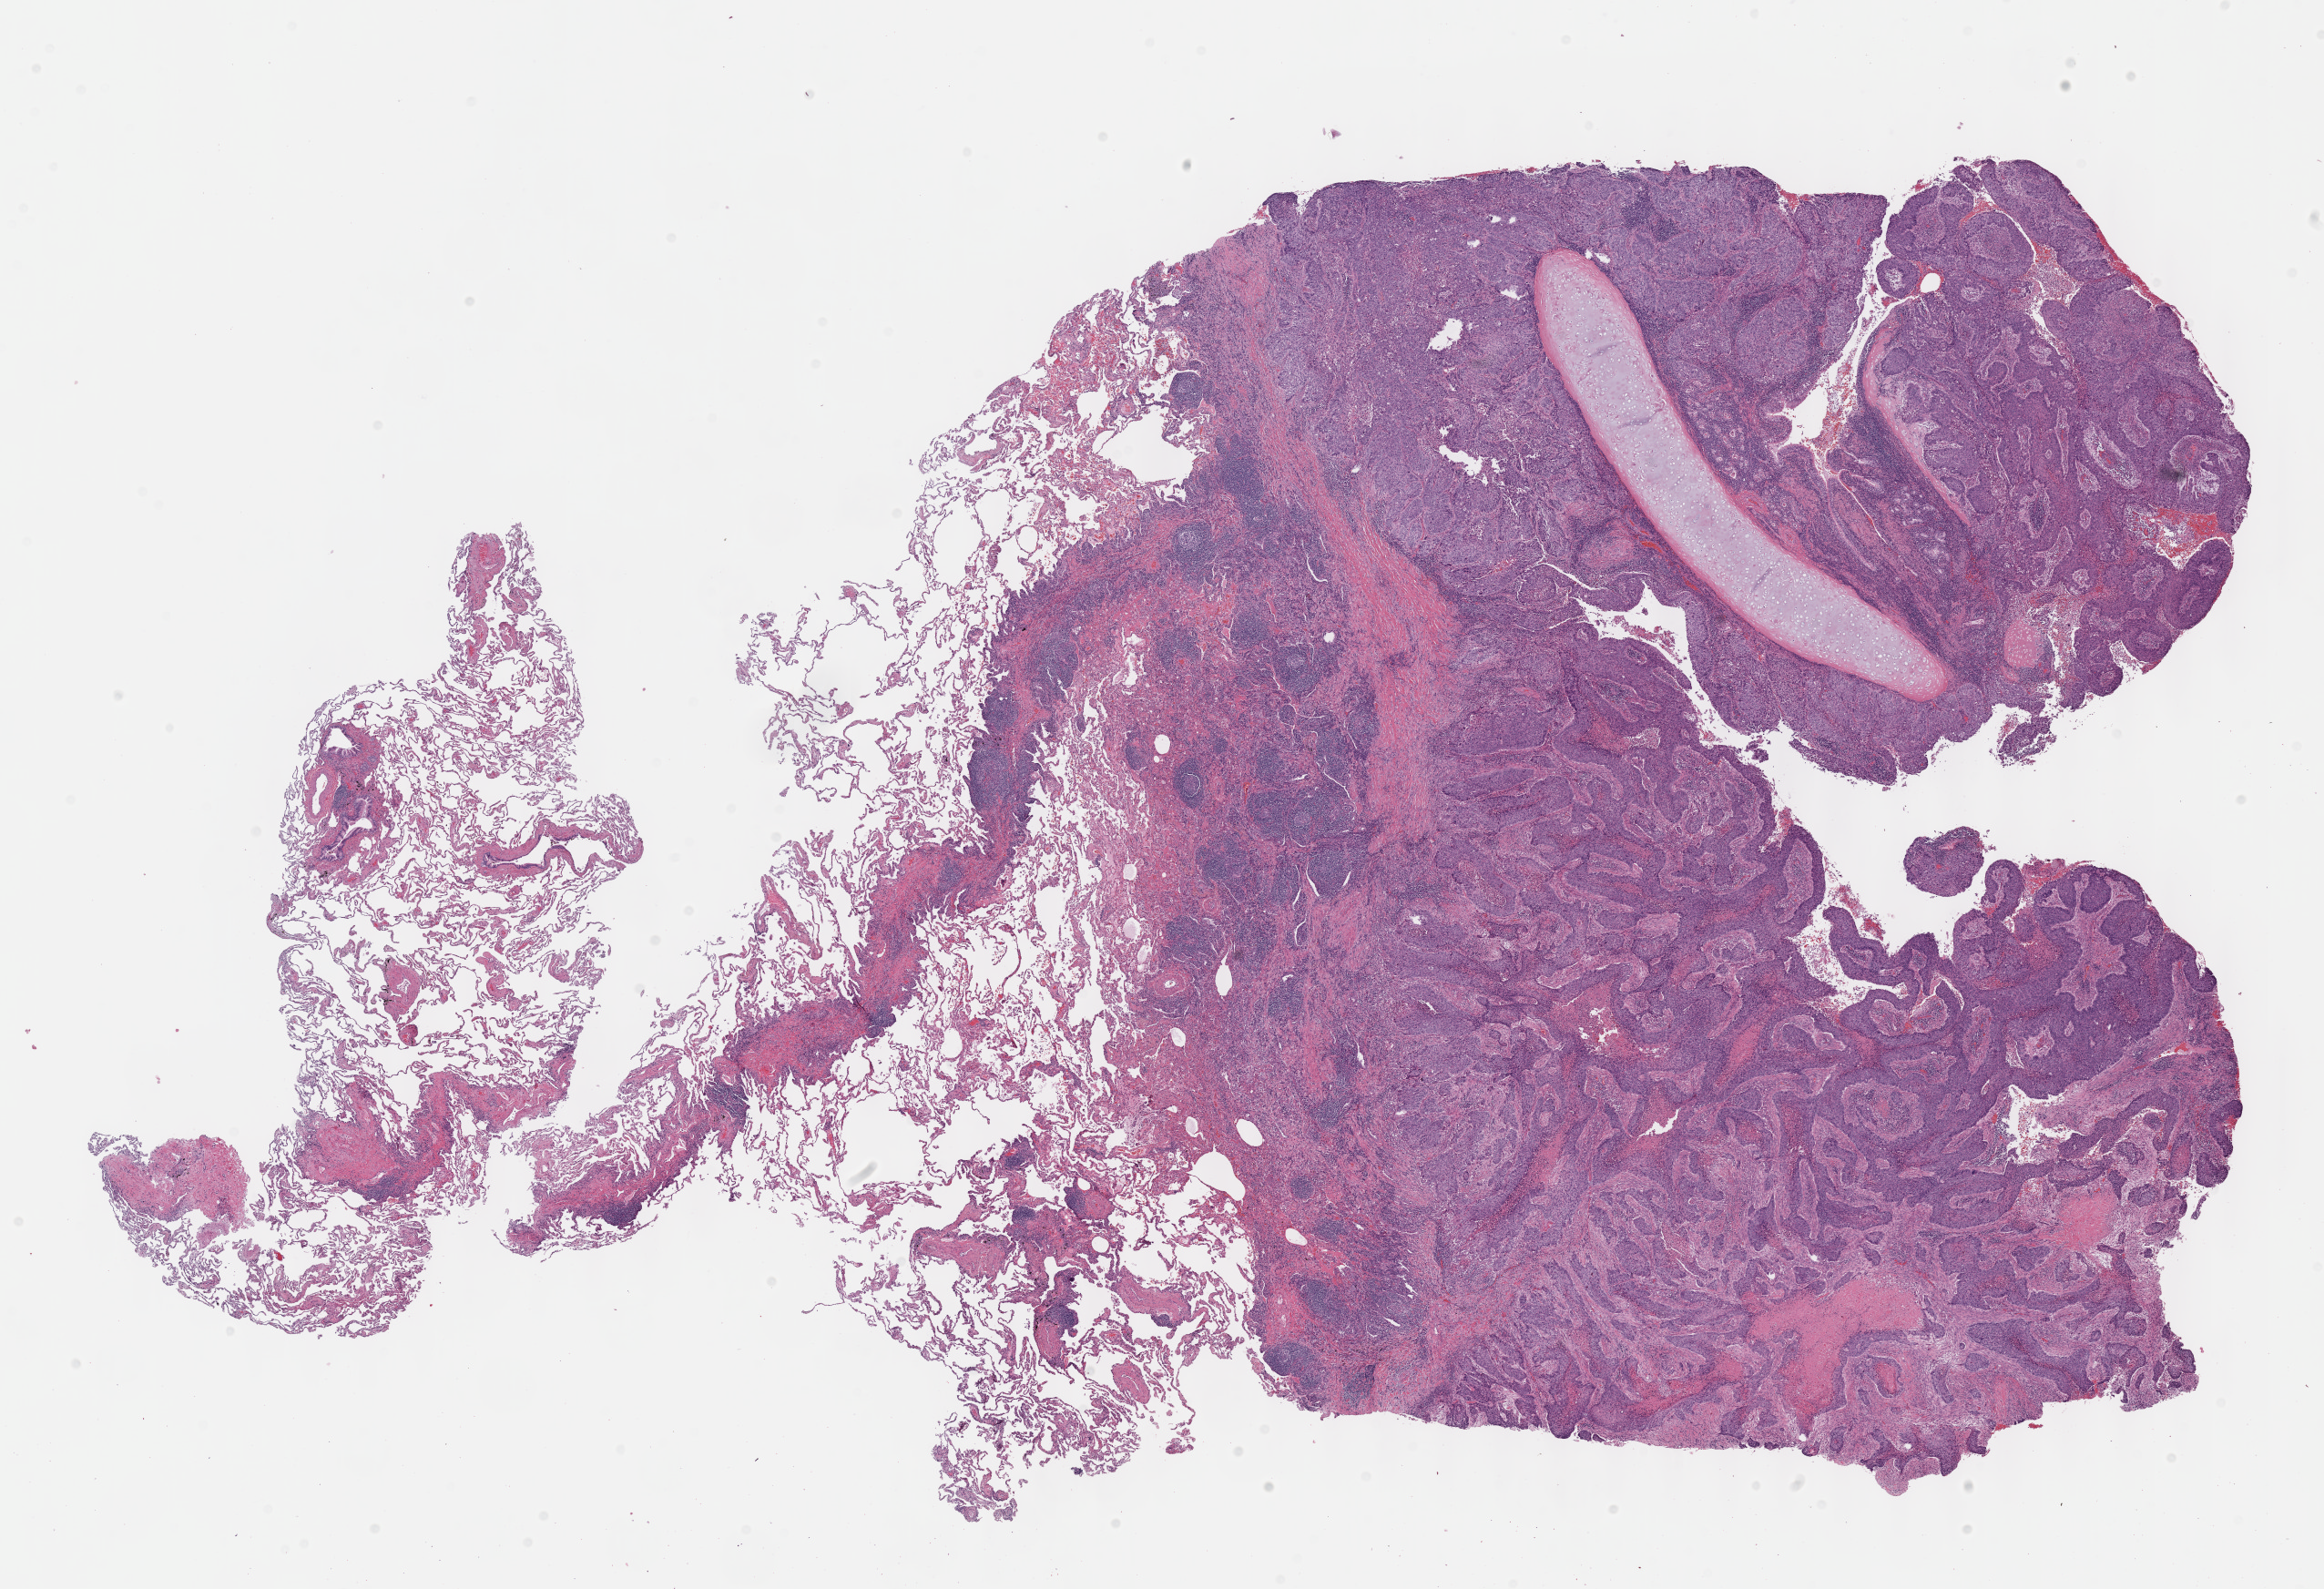
Digitized H&E tissue section (whole slide), a low-resolution overview of the entire scanned area, about 20.6 x 14.1 mm, formalin-fixed paraffin-embedded (FFPE) diagnostic section, primary tumour sample from the lung. Male, age 64 years at initial diagnosis.
- TNM: T2 N0 M0
- AJCC pathologic stage: IB (6th edition)
- pathologic diagnosis: Squamous cell carcinoma, NOS (lower lobe, lung)